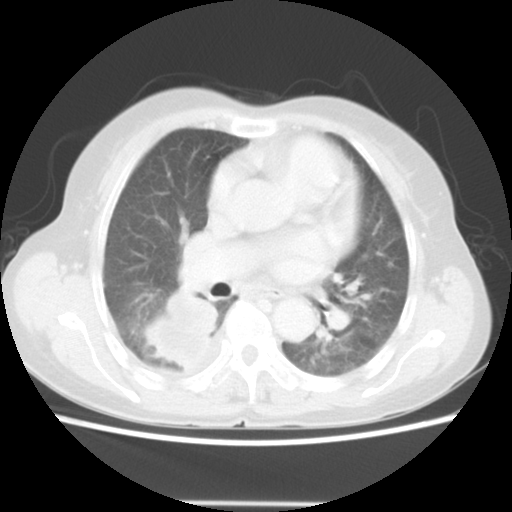
Chest CT, one axial slice. Position 28 of 52 along the scan axis. Reconstruction kernel STANDARD. 140 kVp. Lung window (W 1500 / L -600 HU). 5 mm slice thickness. 512 × 512 image matrix, field of view 337 × 337 mm. Female patient, age 67 years. From the clinical record (not read from this slice): clinical TNM (as recorded): T3 N1 M1.
Outlined on this slice (bounding box drawn by a radiologist):
- lung tumour (recorded histology: adenocarcinoma): bounding box [x1, y1, x2, y2] px = [142, 291, 224, 371]